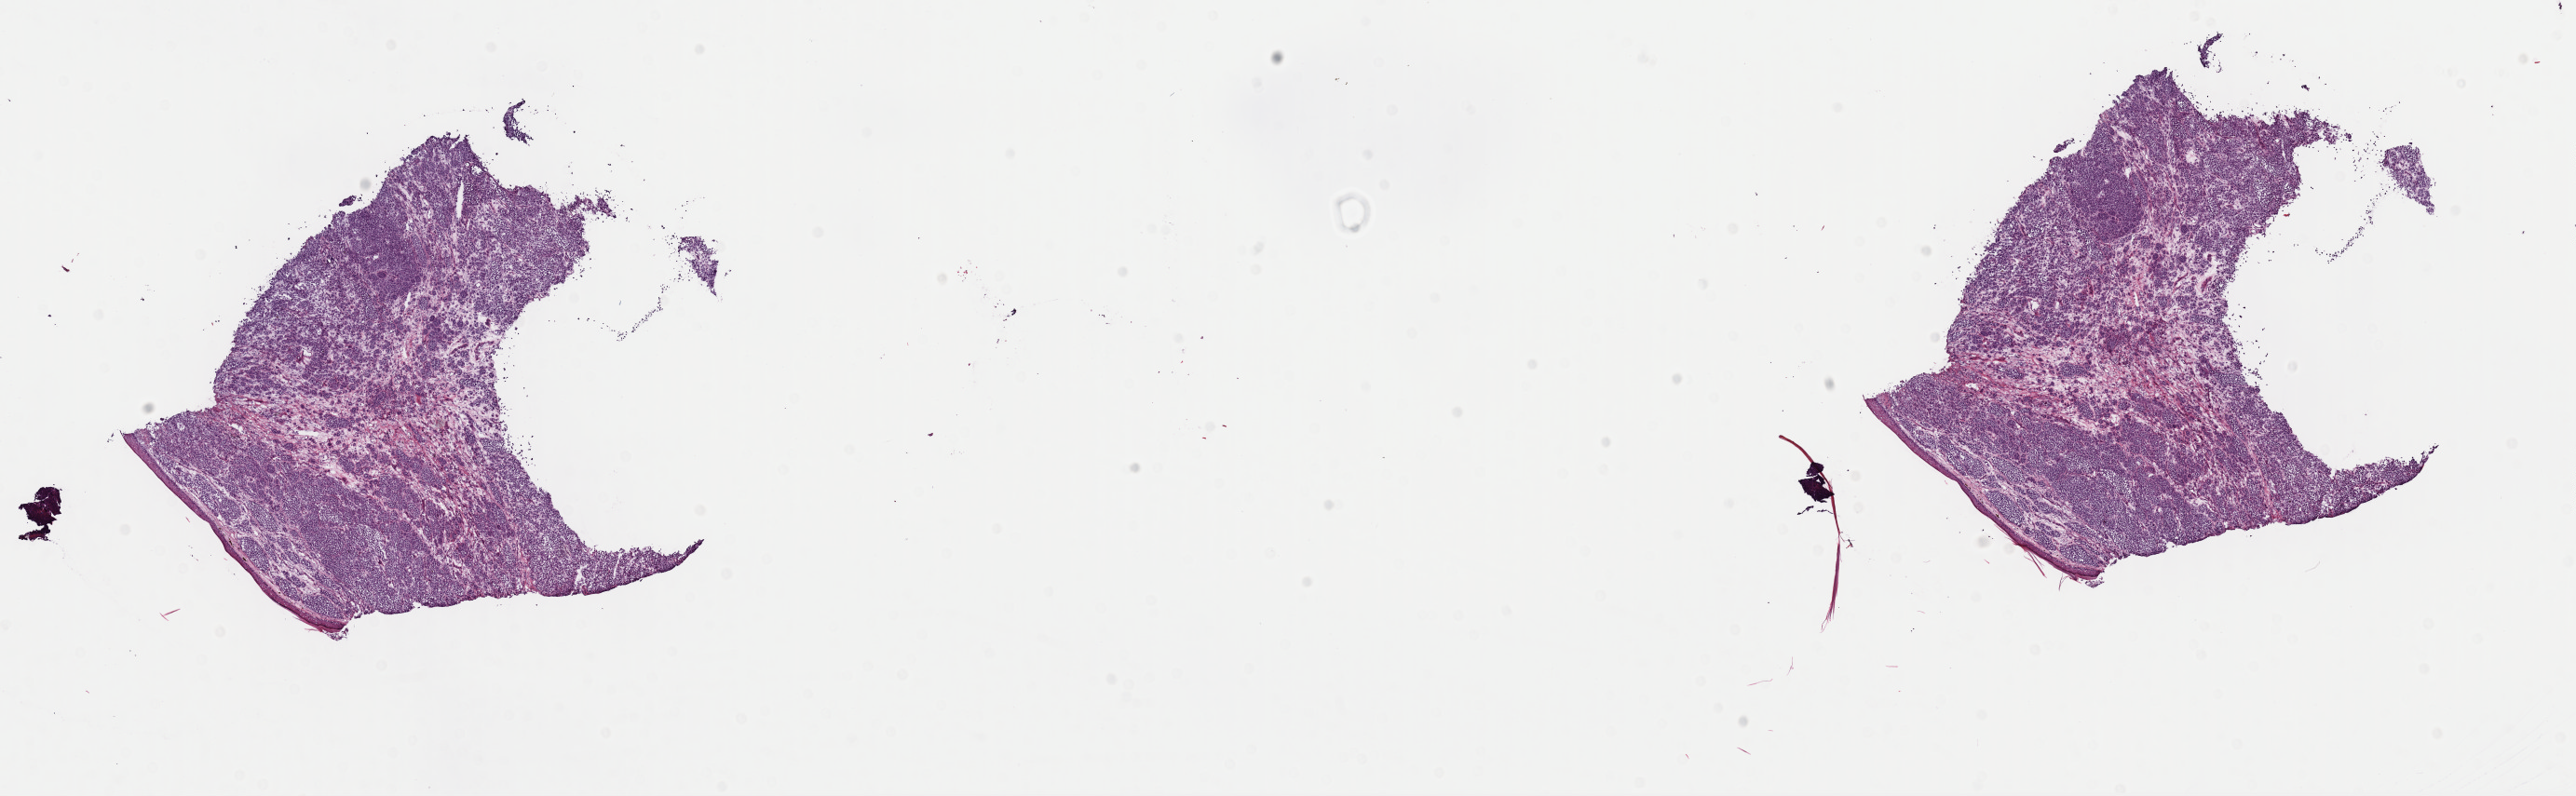
Whole-slide histology image, Hematoxylin and eosin (H&E) stained — a low-resolution overview of the entire scanned area, about 21.9 x 6.8 mm (acquisition: 40x scan); frozen section; primary tumour sample from the skin. Patient sex: female. Slide review estimates, as recorded: tumour cells 95%, tumour nuclei 80%, normal cells 5%, stromal cells 0%, necrosis 0%. Inflammatory infiltration, as recorded: lymphocyte infiltration 2%, monocyte infiltration 0%, neutrophil infiltration 0%.
- pathologic diagnosis: Malignant melanoma, NOS